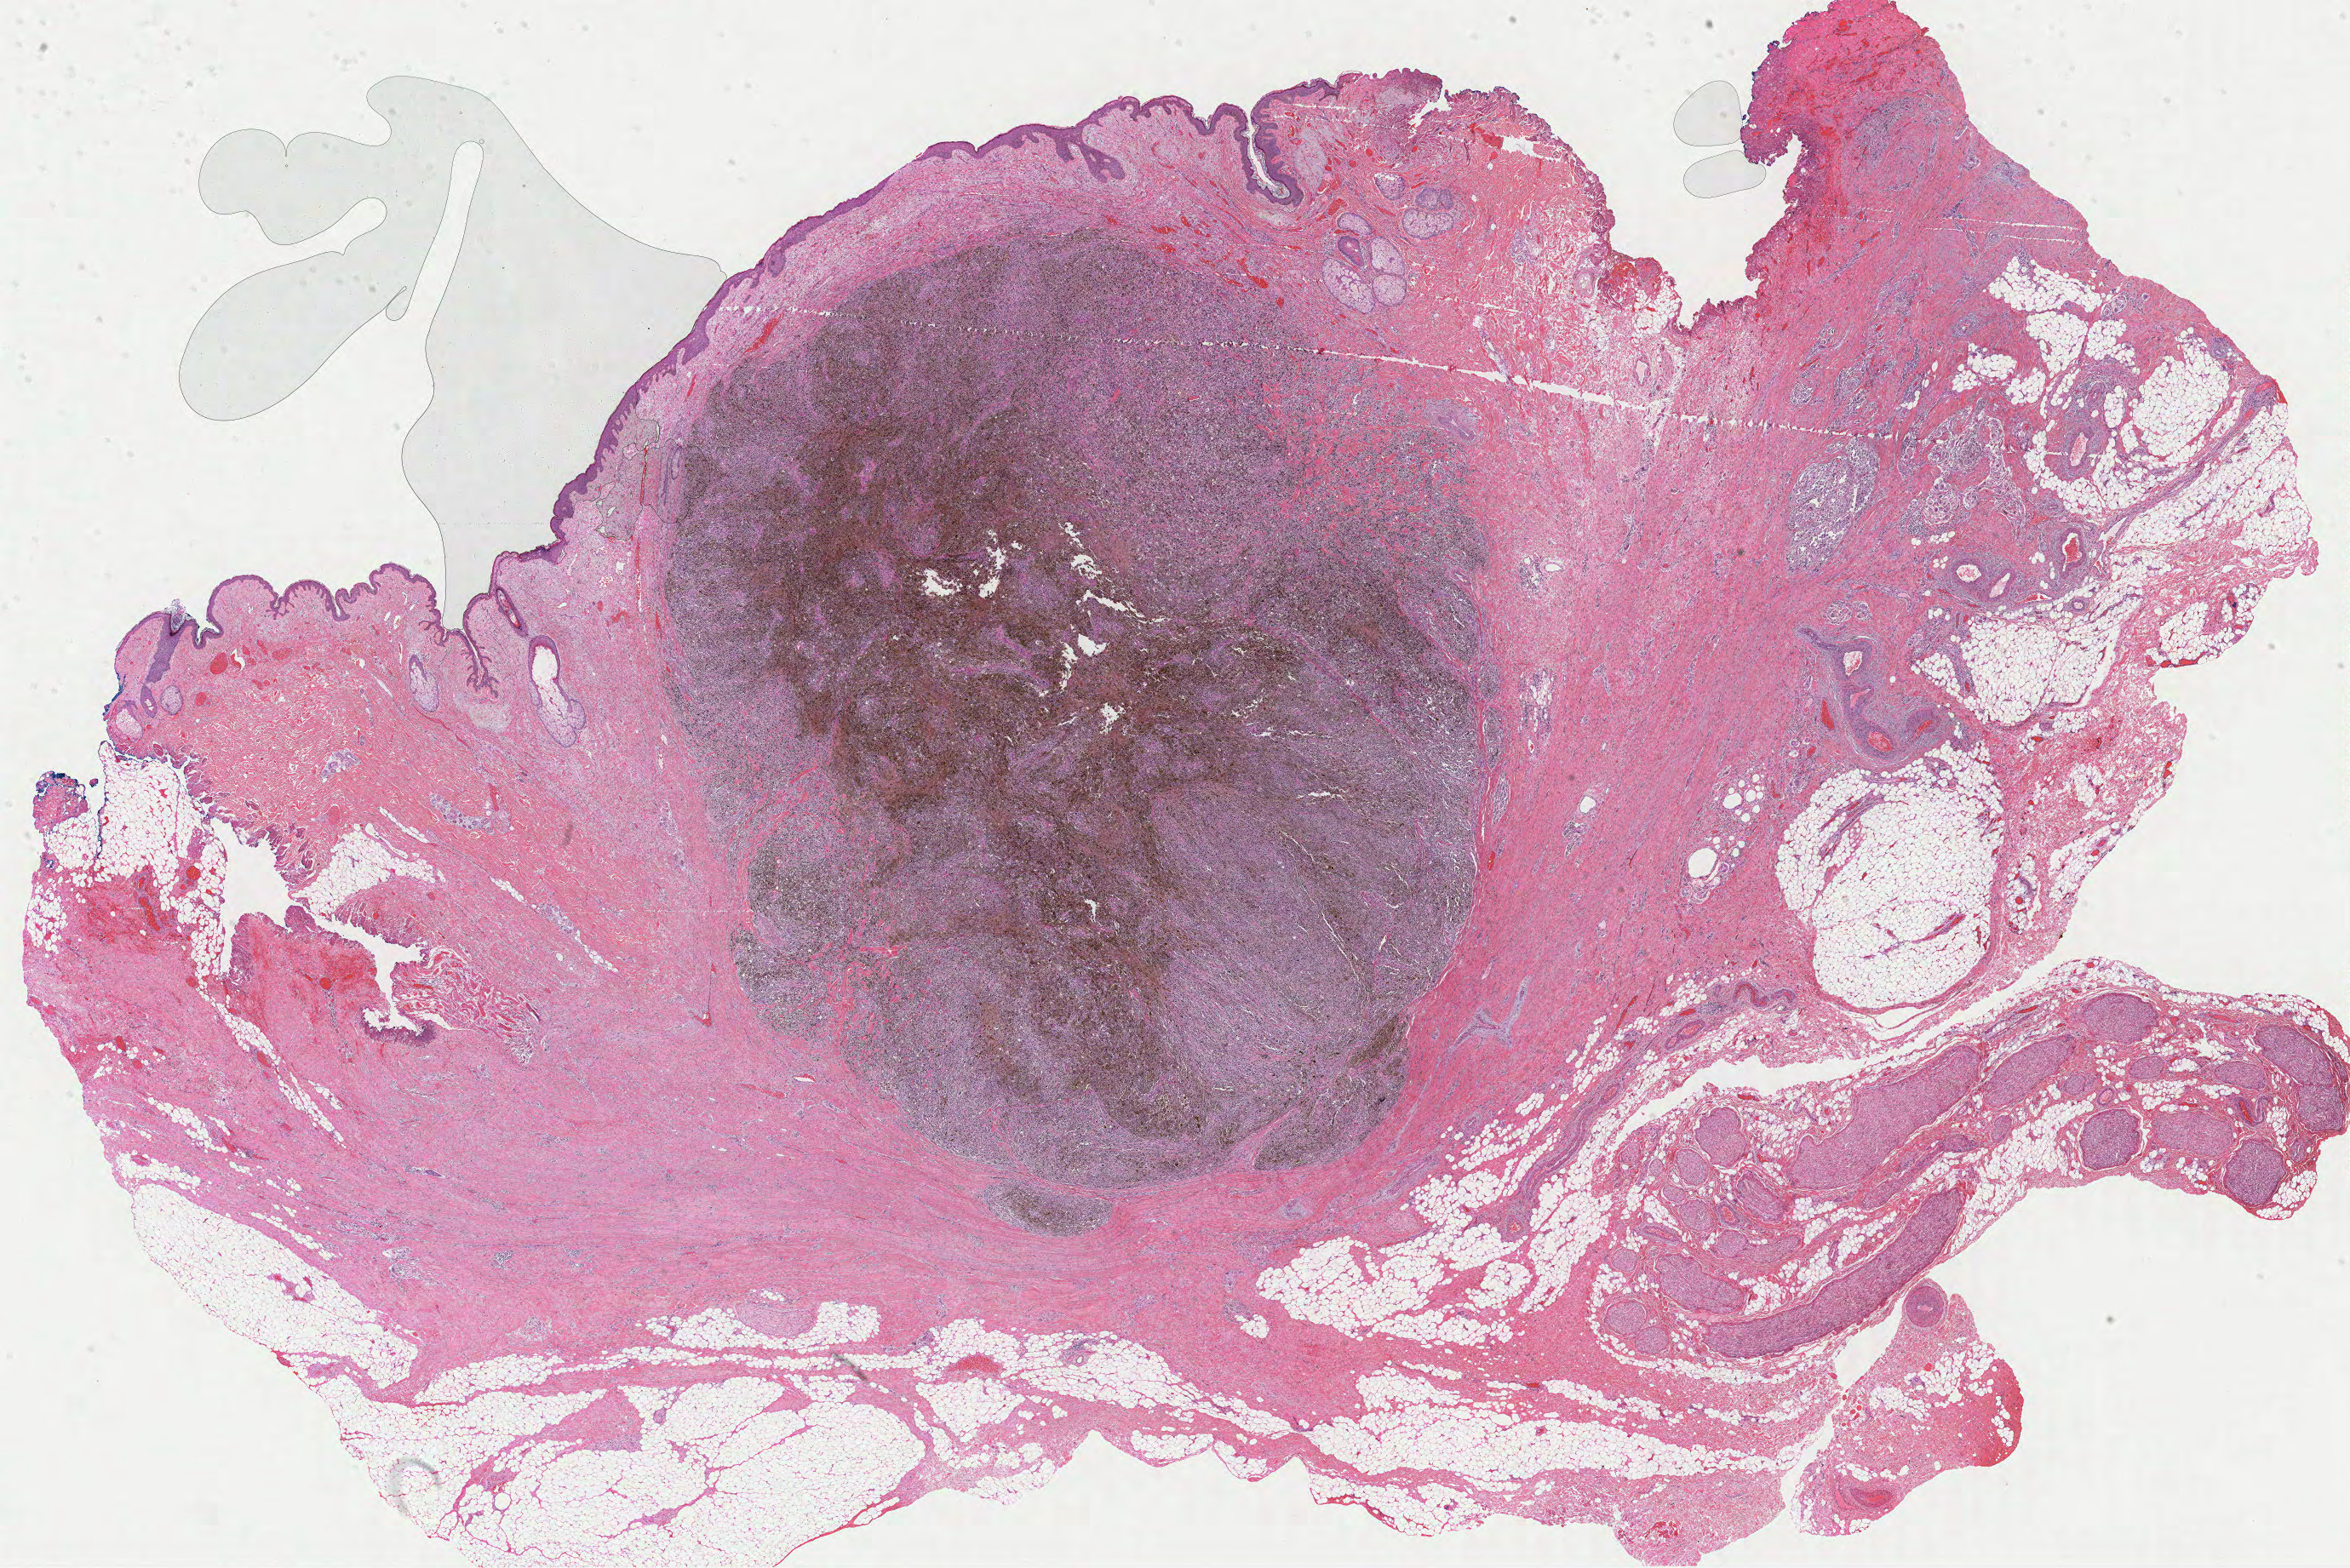
Whole-slide histology image, H&E, shown as a low-resolution overview of the whole scanned area (about 22.1 x 14.8 mm, from a 40x scan). FFPE section. Metastatic tumour sample. Male patient; age at initial diagnosis 68 years.
• this section: metastatic tumour tissue
• patient diagnosis: Malignant melanoma, NOS